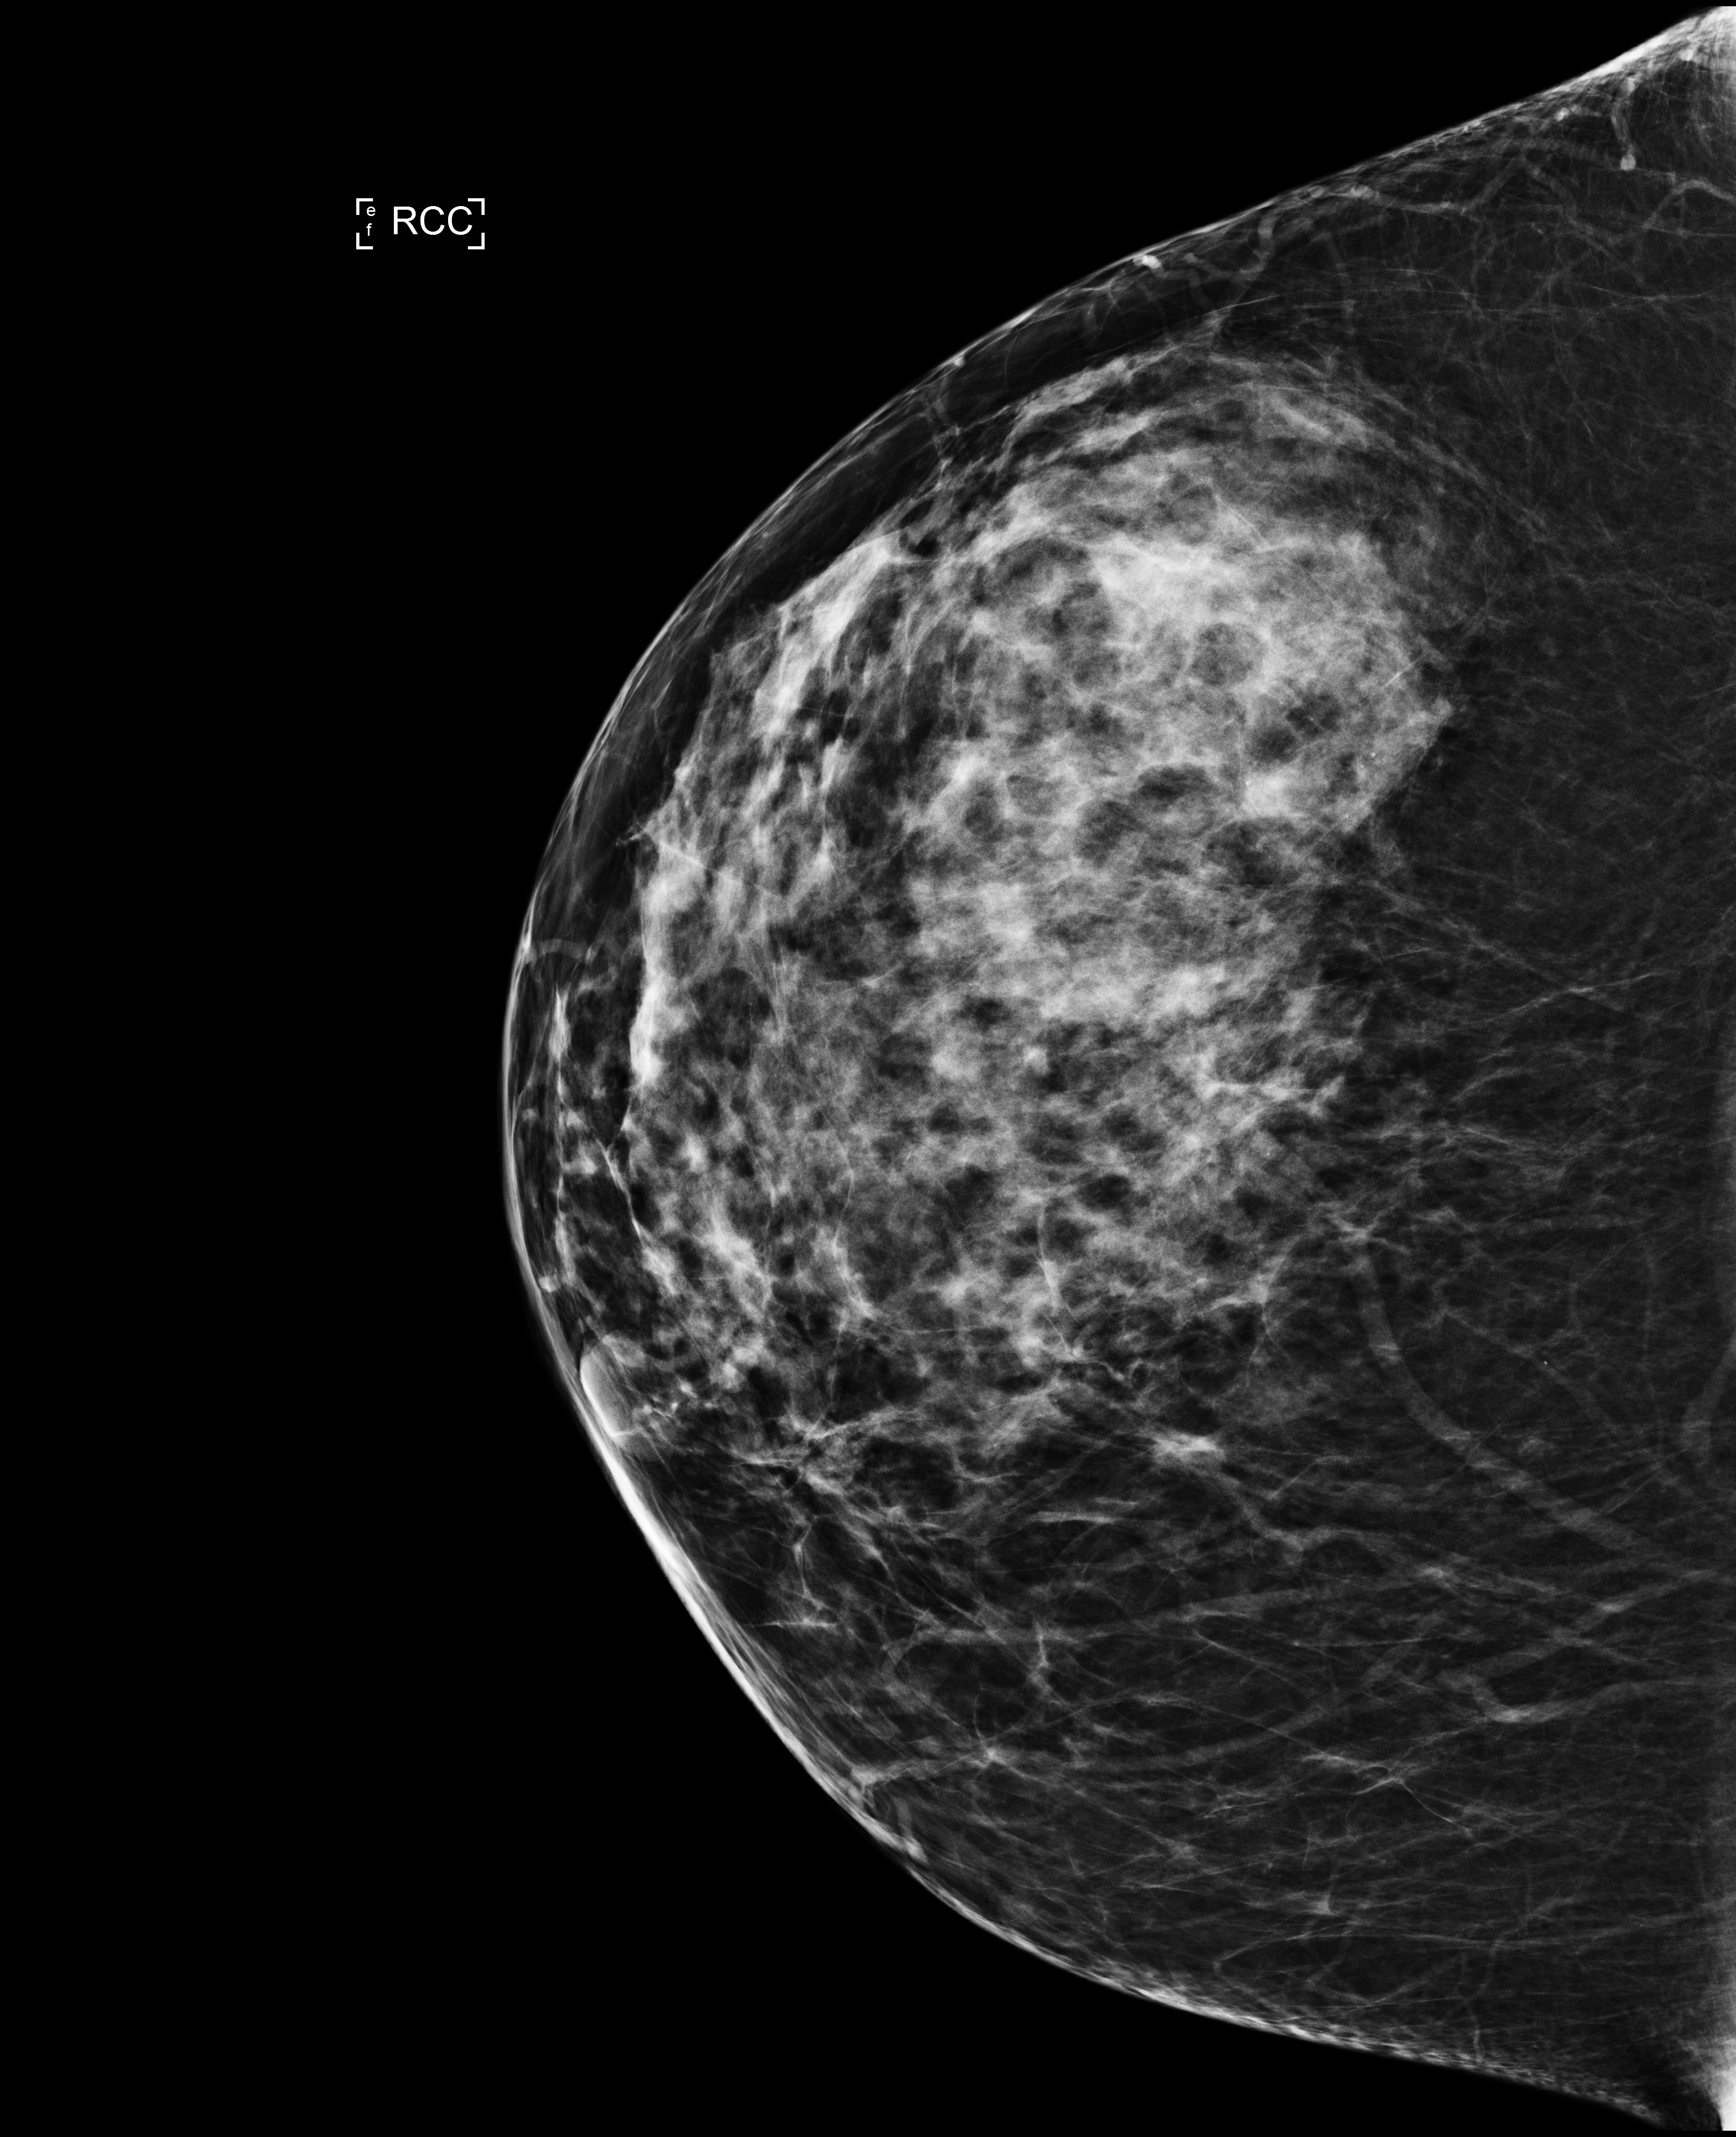
Full-field digital mammogram (FFDM), right breast, craniocaudal (CC) view, screening examination, system: Selenia Dimensions. Patient: female, 49 years.
Breast density at the screening exam (both breasts): heterogeneously dense (BI-RADS density category c). Final BI-RADS category for the screening round (tomosynthesis exam, both breasts): category 1. Recall: no recall after this screen.